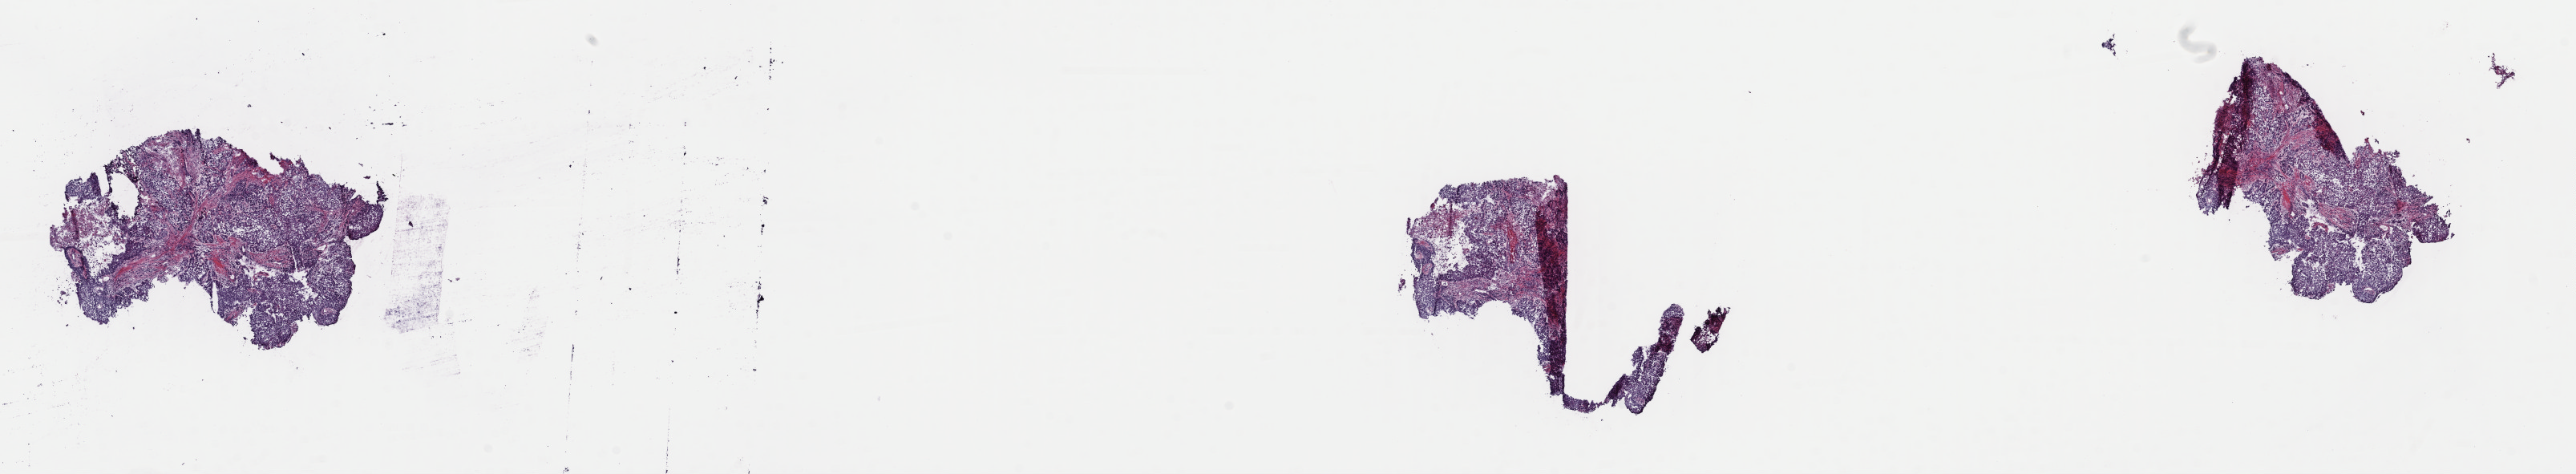
H&E-stained whole-slide image — low-resolution overview of the scanned area, about 25.3 x 4.7 mm (acquisition: 40x scan). Frozen section from the top of the tissue portion. Lung, primary tumour sample. Patient: male, age at initial diagnosis 79 years. Composition of this section per pathologist review: tumour cells 70%, tumour nuclei 90%, normal cells 0%, stromal cells 20%, necrosis 10%. Infiltration values recorded for this section: lymphocyte infiltration 4%, monocyte infiltration 4%, neutrophil infiltration 0%.
• AJCC pathologic stage: IIB (6th edition)
• diagnosis: Squamous cell carcinoma, NOS